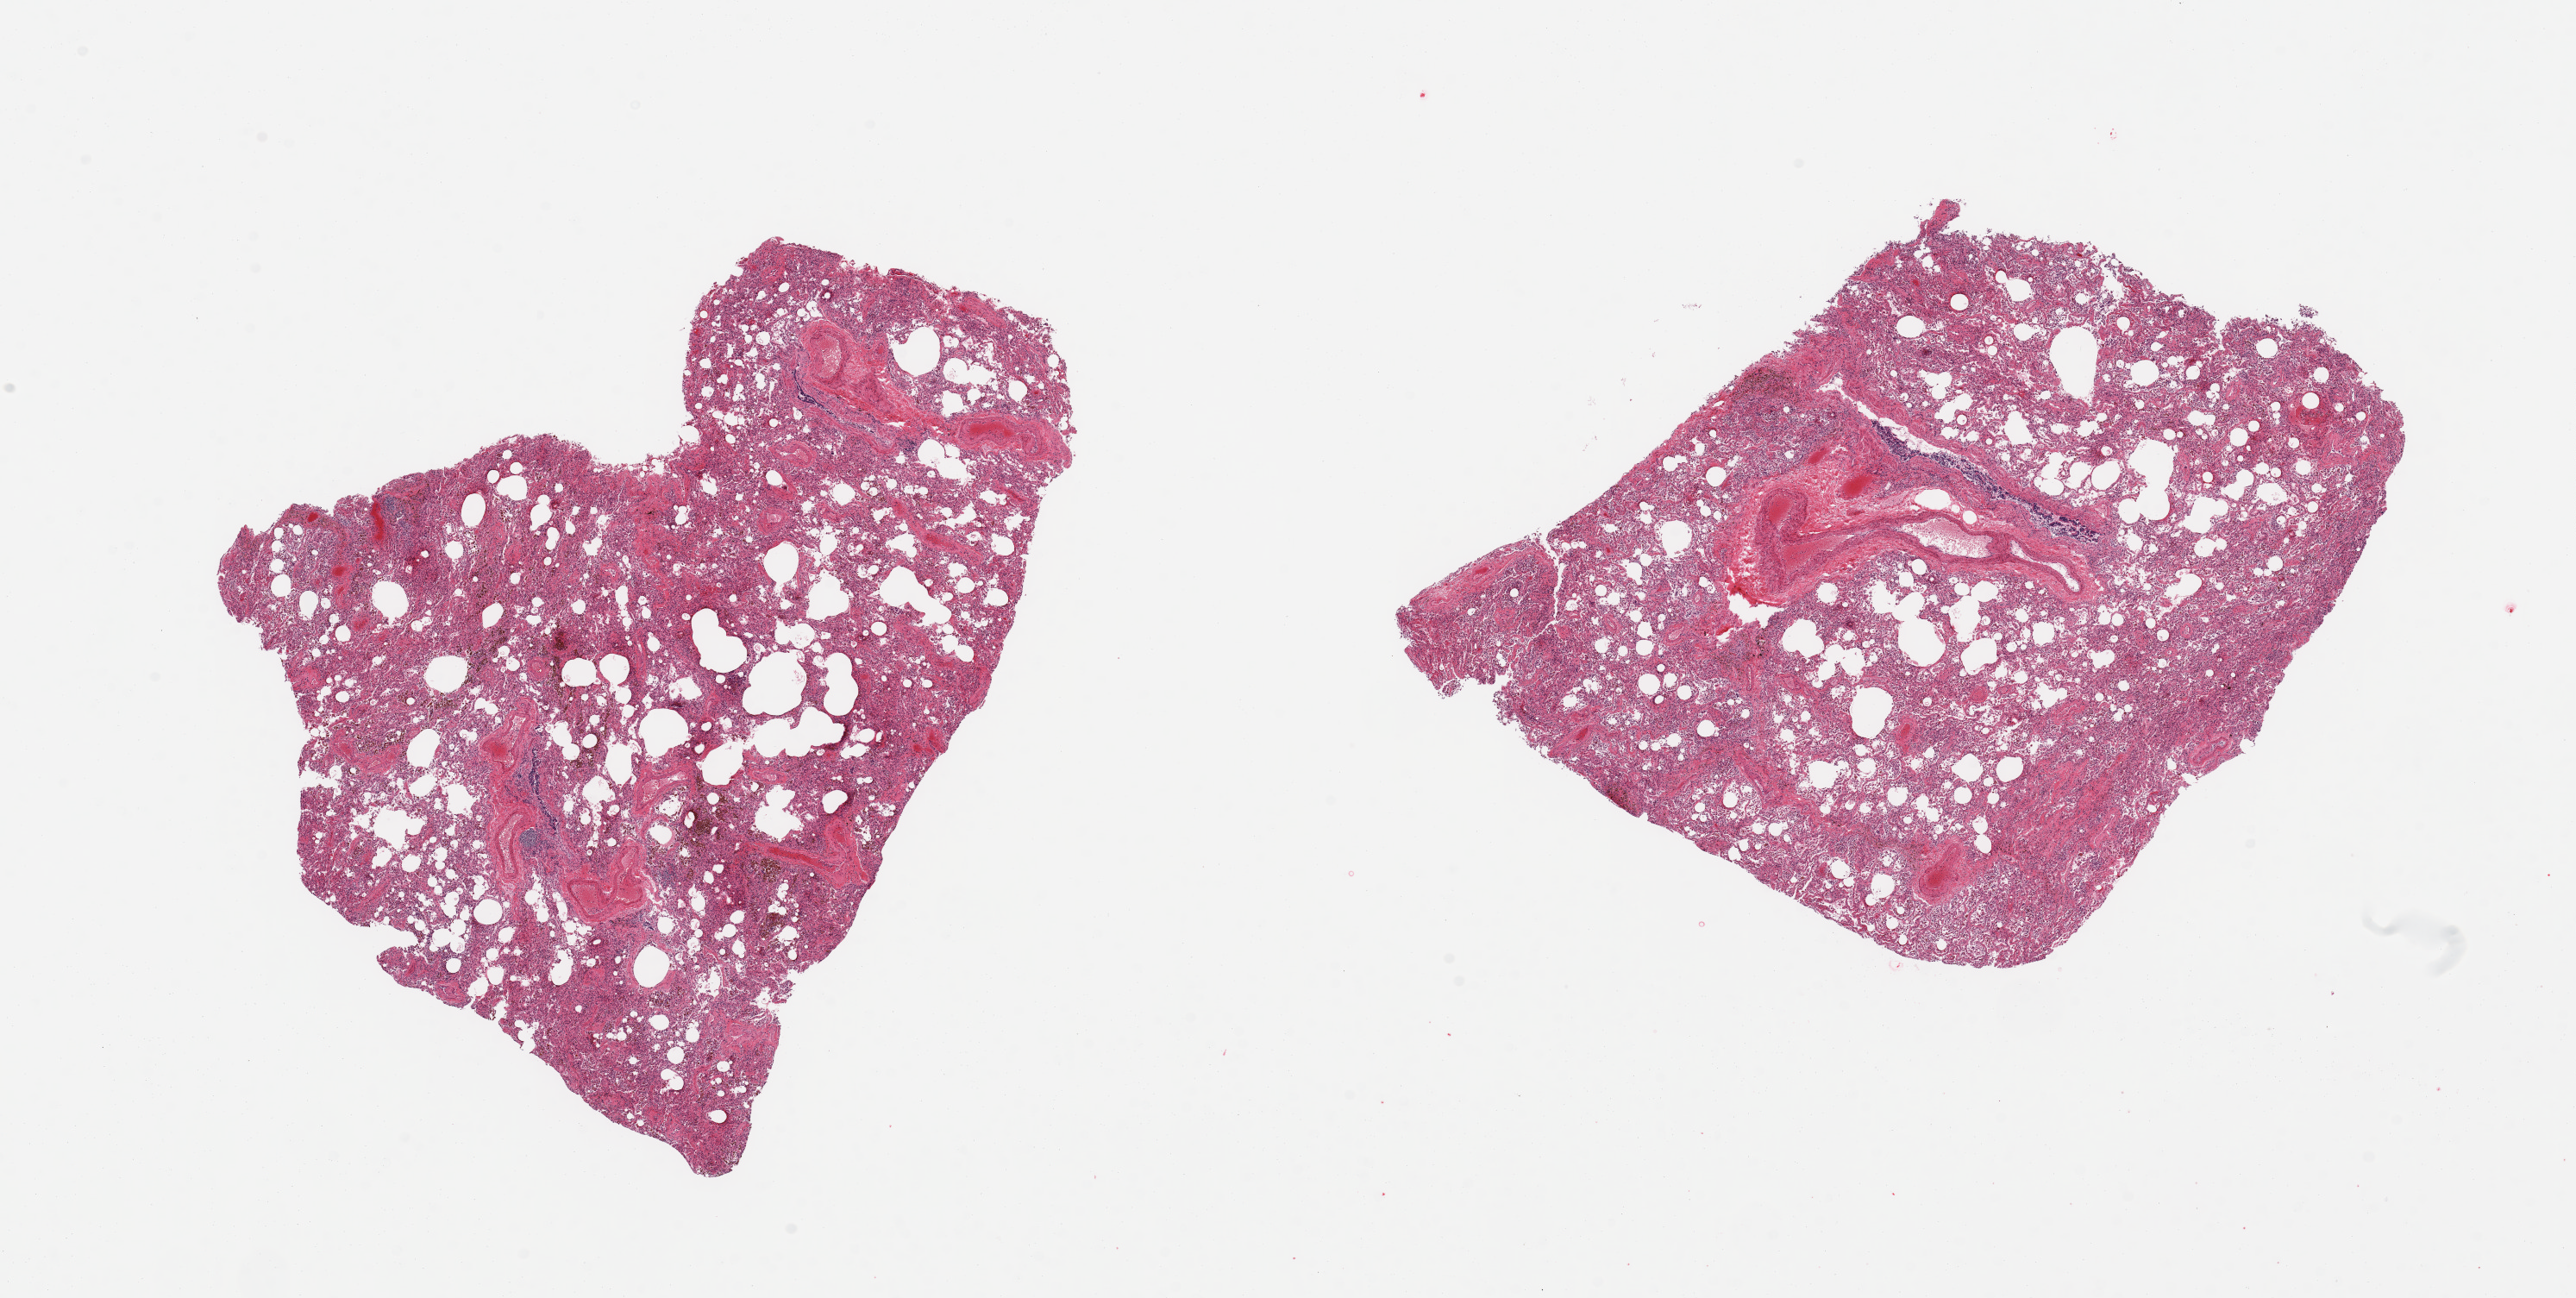
Digitized hematoxylin and eosin (H&E)-stained section — a low-resolution overview of the entire scanned area, about 23.6 x 11.9 mm. PAXgene-fixed paraffin-embedded (PFPE) section. Section of lung (target tissue). Tissue donor sample.
* reviewer comment on this tissue sample: 2 pieces; numerous pigmented alveolar macrophages (heart failure cells)